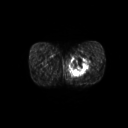
FDG PET of an extremity soft-tissue mass (from a PET/CT study), one axial slice; slice 27 of 267 in the series (ordered by position); 128 × 128 image matrix. Patient: male, 59 years. Case-level facts recorded for this patient, not image findings: histological type: pleiomorphic liposarcoma; grade: high; site of the primary tumour: left thigh.
Structures marked on this image (expert contour drawn on MRI and transferred to this co-registered scan by the dataset authors):
- gross tumour volume including surrounding oedema: bounding box [x1, y1, x2, y2] px = [69, 56, 91, 77]
- gross tumour volume (mass): [70, 57, 89, 75]